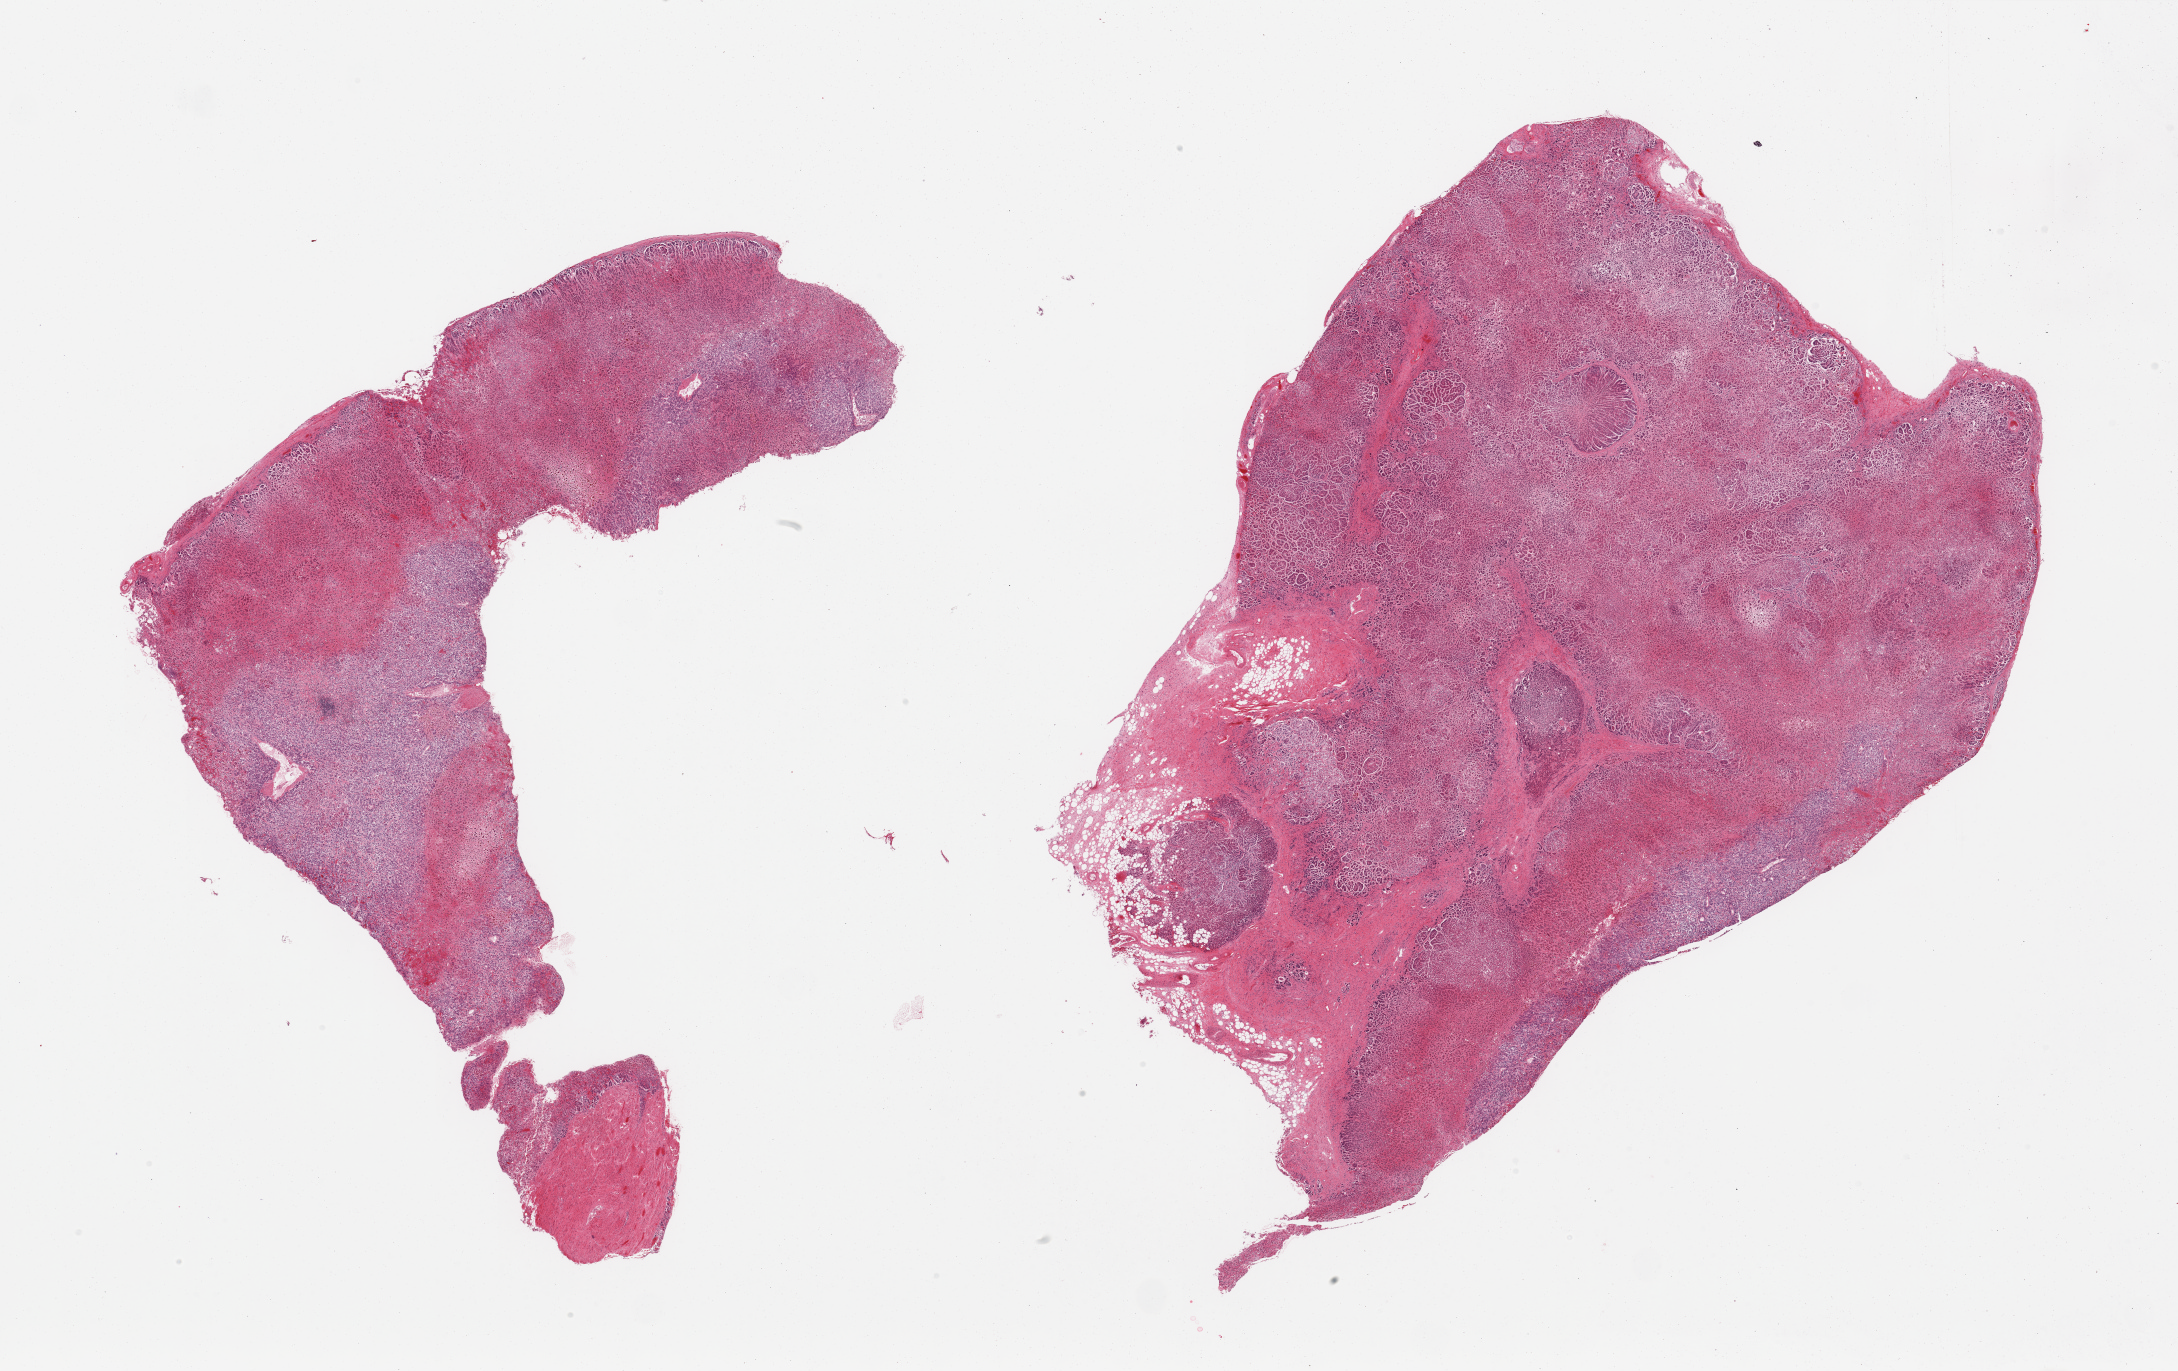
Digitized H&E-stained section — a low-resolution overview of the entire scanned area, about 34.5 x 21.7 mm; PAXgene-fixed paraffin-embedded (PFPE) section; section of adrenal gland (target tissue); tissue donor sample.
Pathologist's review note for this sample: 2 pieces.